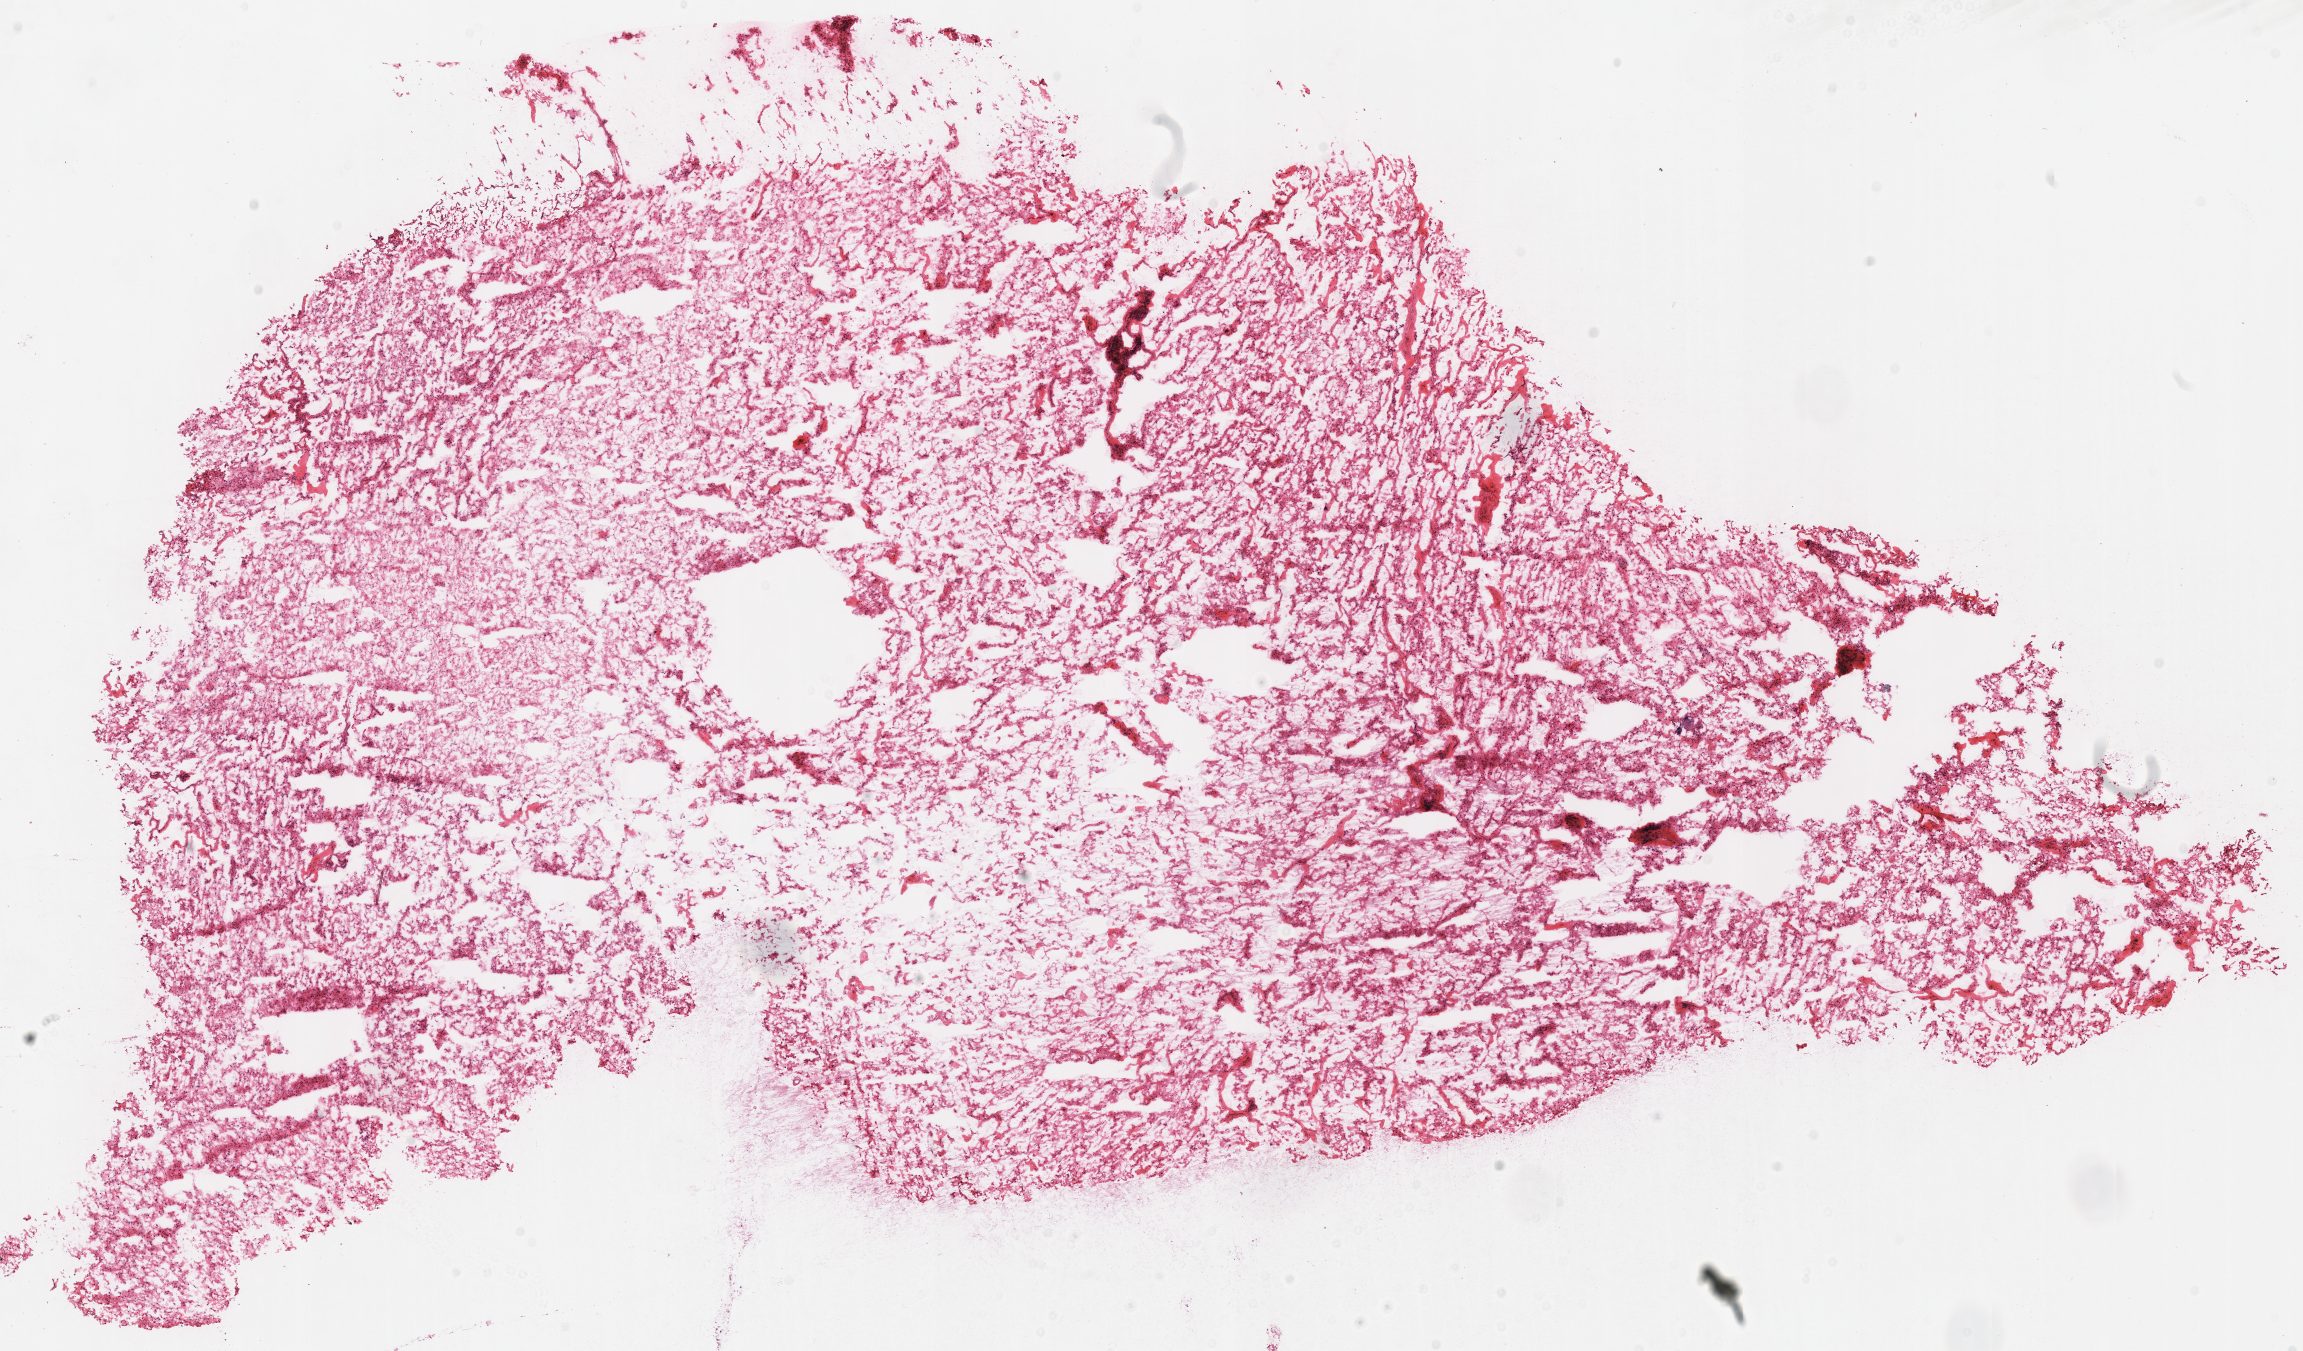
Digitized H&E-stained tissue section (whole slide) — low-resolution overview of the scanned area, about 18.1 x 10.6 mm (slide scanned at 40x); frozen section; kidney, primary tumour sample. Female patient; age at initial diagnosis 65 years. Composition of this section per pathologist review: tumour cells 100%, tumour nuclei 90%, normal cells 0%, stromal cells 0%, necrosis 0%. Infiltration values recorded for this section: lymphocyte infiltration 0%, monocyte infiltration 0%, neutrophil infiltration 0%.
Histologic diagnosis: Renal cell carcinoma, chromophobe type. AJCC pathologic stage: II (6th edition).